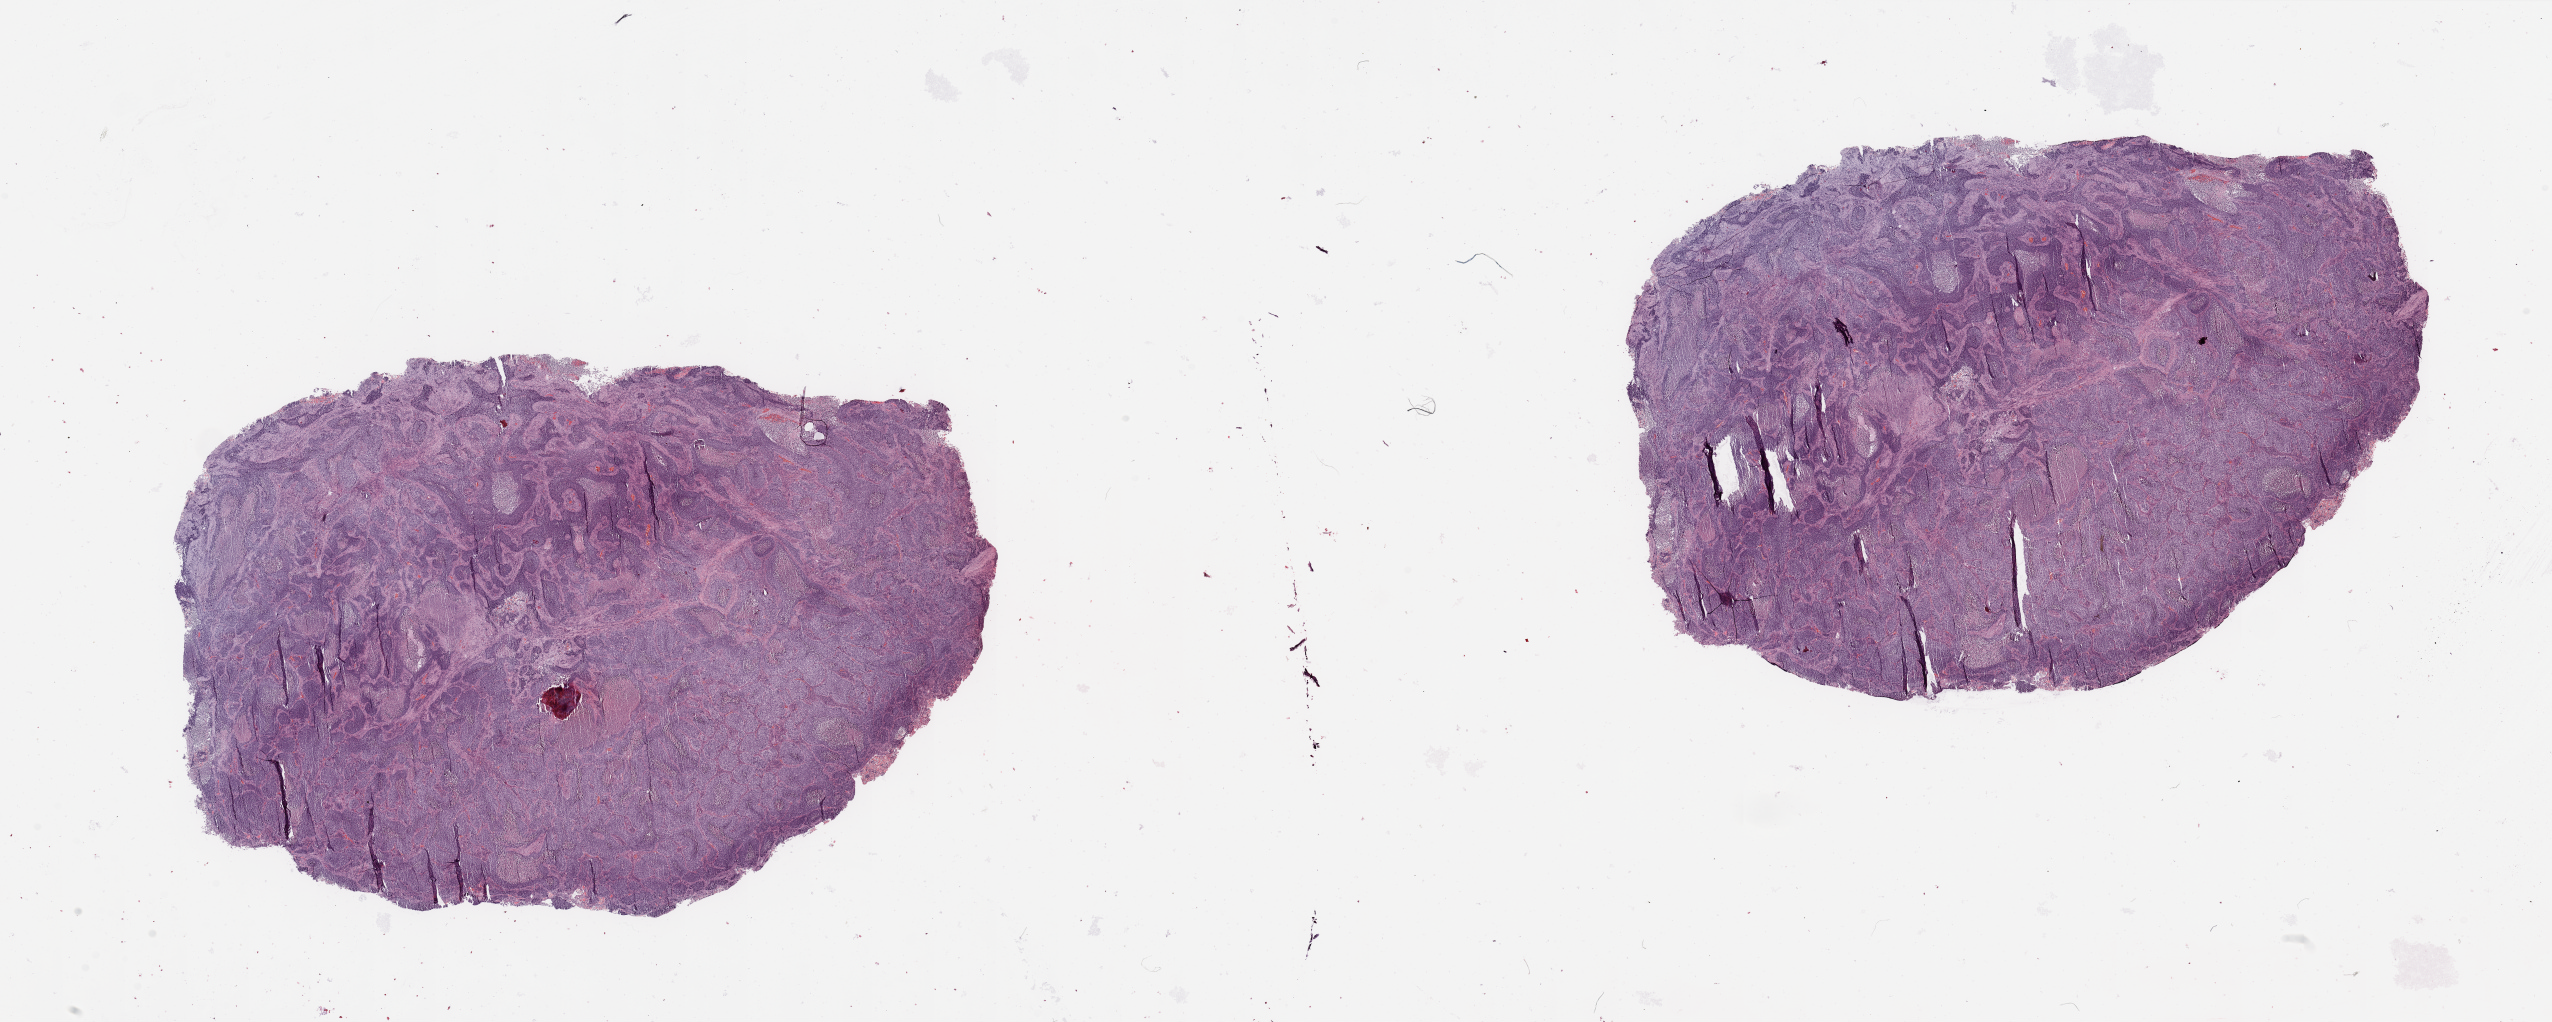
Whole-slide histology image, H&E-stained, whole scanned area (about 40.4 x 16.2 mm, acquisition: 20x scan) shown as a low-resolution overview. Tumour tissue sample, lung. 73-year-old male patient. Histologic grade: G3 (poorly differentiated).
• AJCC pathologic stage: IIB
• primary tumour site (as recorded): left upper lobe
• diagnosis: Squamous cell carcinoma, NOS